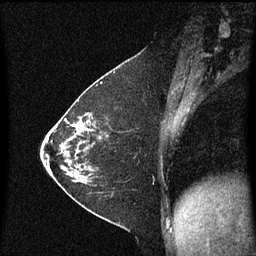
Breast MRI (dynamic contrast-enhanced), one sagittal slice. Position 27 of 60 along the scan axis. Dynamic contrast-enhanced series, image 2 of 3 at this slice position (ordered by acquisition). 1.5 T. TE 4.2 ms, TR 8.4 ms. 2 mm slice thickness. 256 × 256 image matrix, field of view 200 × 200 mm. Female patient, age 36 years. Case-level facts recorded for this patient, not image findings: setting: breast cancer imaged before/during neoadjuvant chemotherapy; receptor status: HR-positive, HER2-negative.
Outlined on this slice (semi-automatically segmented with operator editing):
- analysis volume of interest (the breast-tissue region the enhancement analysis was run in; not a lesion): box from (x=72, y=116) to (x=109, y=185) px
- tumour enhancement mask (voxels above the 70 % enhancement threshold inside the analysis volume of interest): (x=72, y=116)–(x=91, y=175)